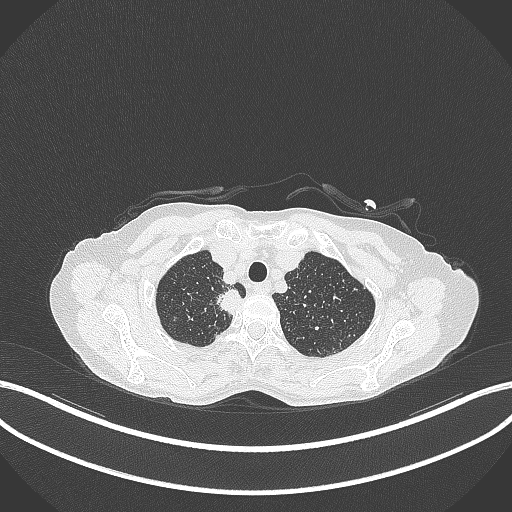
Chest CT, one axial slice; position 324 of 403 along the scan axis; reconstruction kernel B70f; 120 kVp; lung window (W 1500 / L -600 HU); 1 mm slice thickness; 512 × 512 image matrix, field of view 400 × 400 mm. Female patient, age 75 years. Case-level facts recorded for this patient, not image findings: clinical TNM (as recorded): T1c N1 M1.
Annotated regions visible in this slice (bounding box drawn by a radiologist):
- lung tumour (recorded histology: adenocarcinoma): box from (x=215, y=287) to (x=244, y=315) px